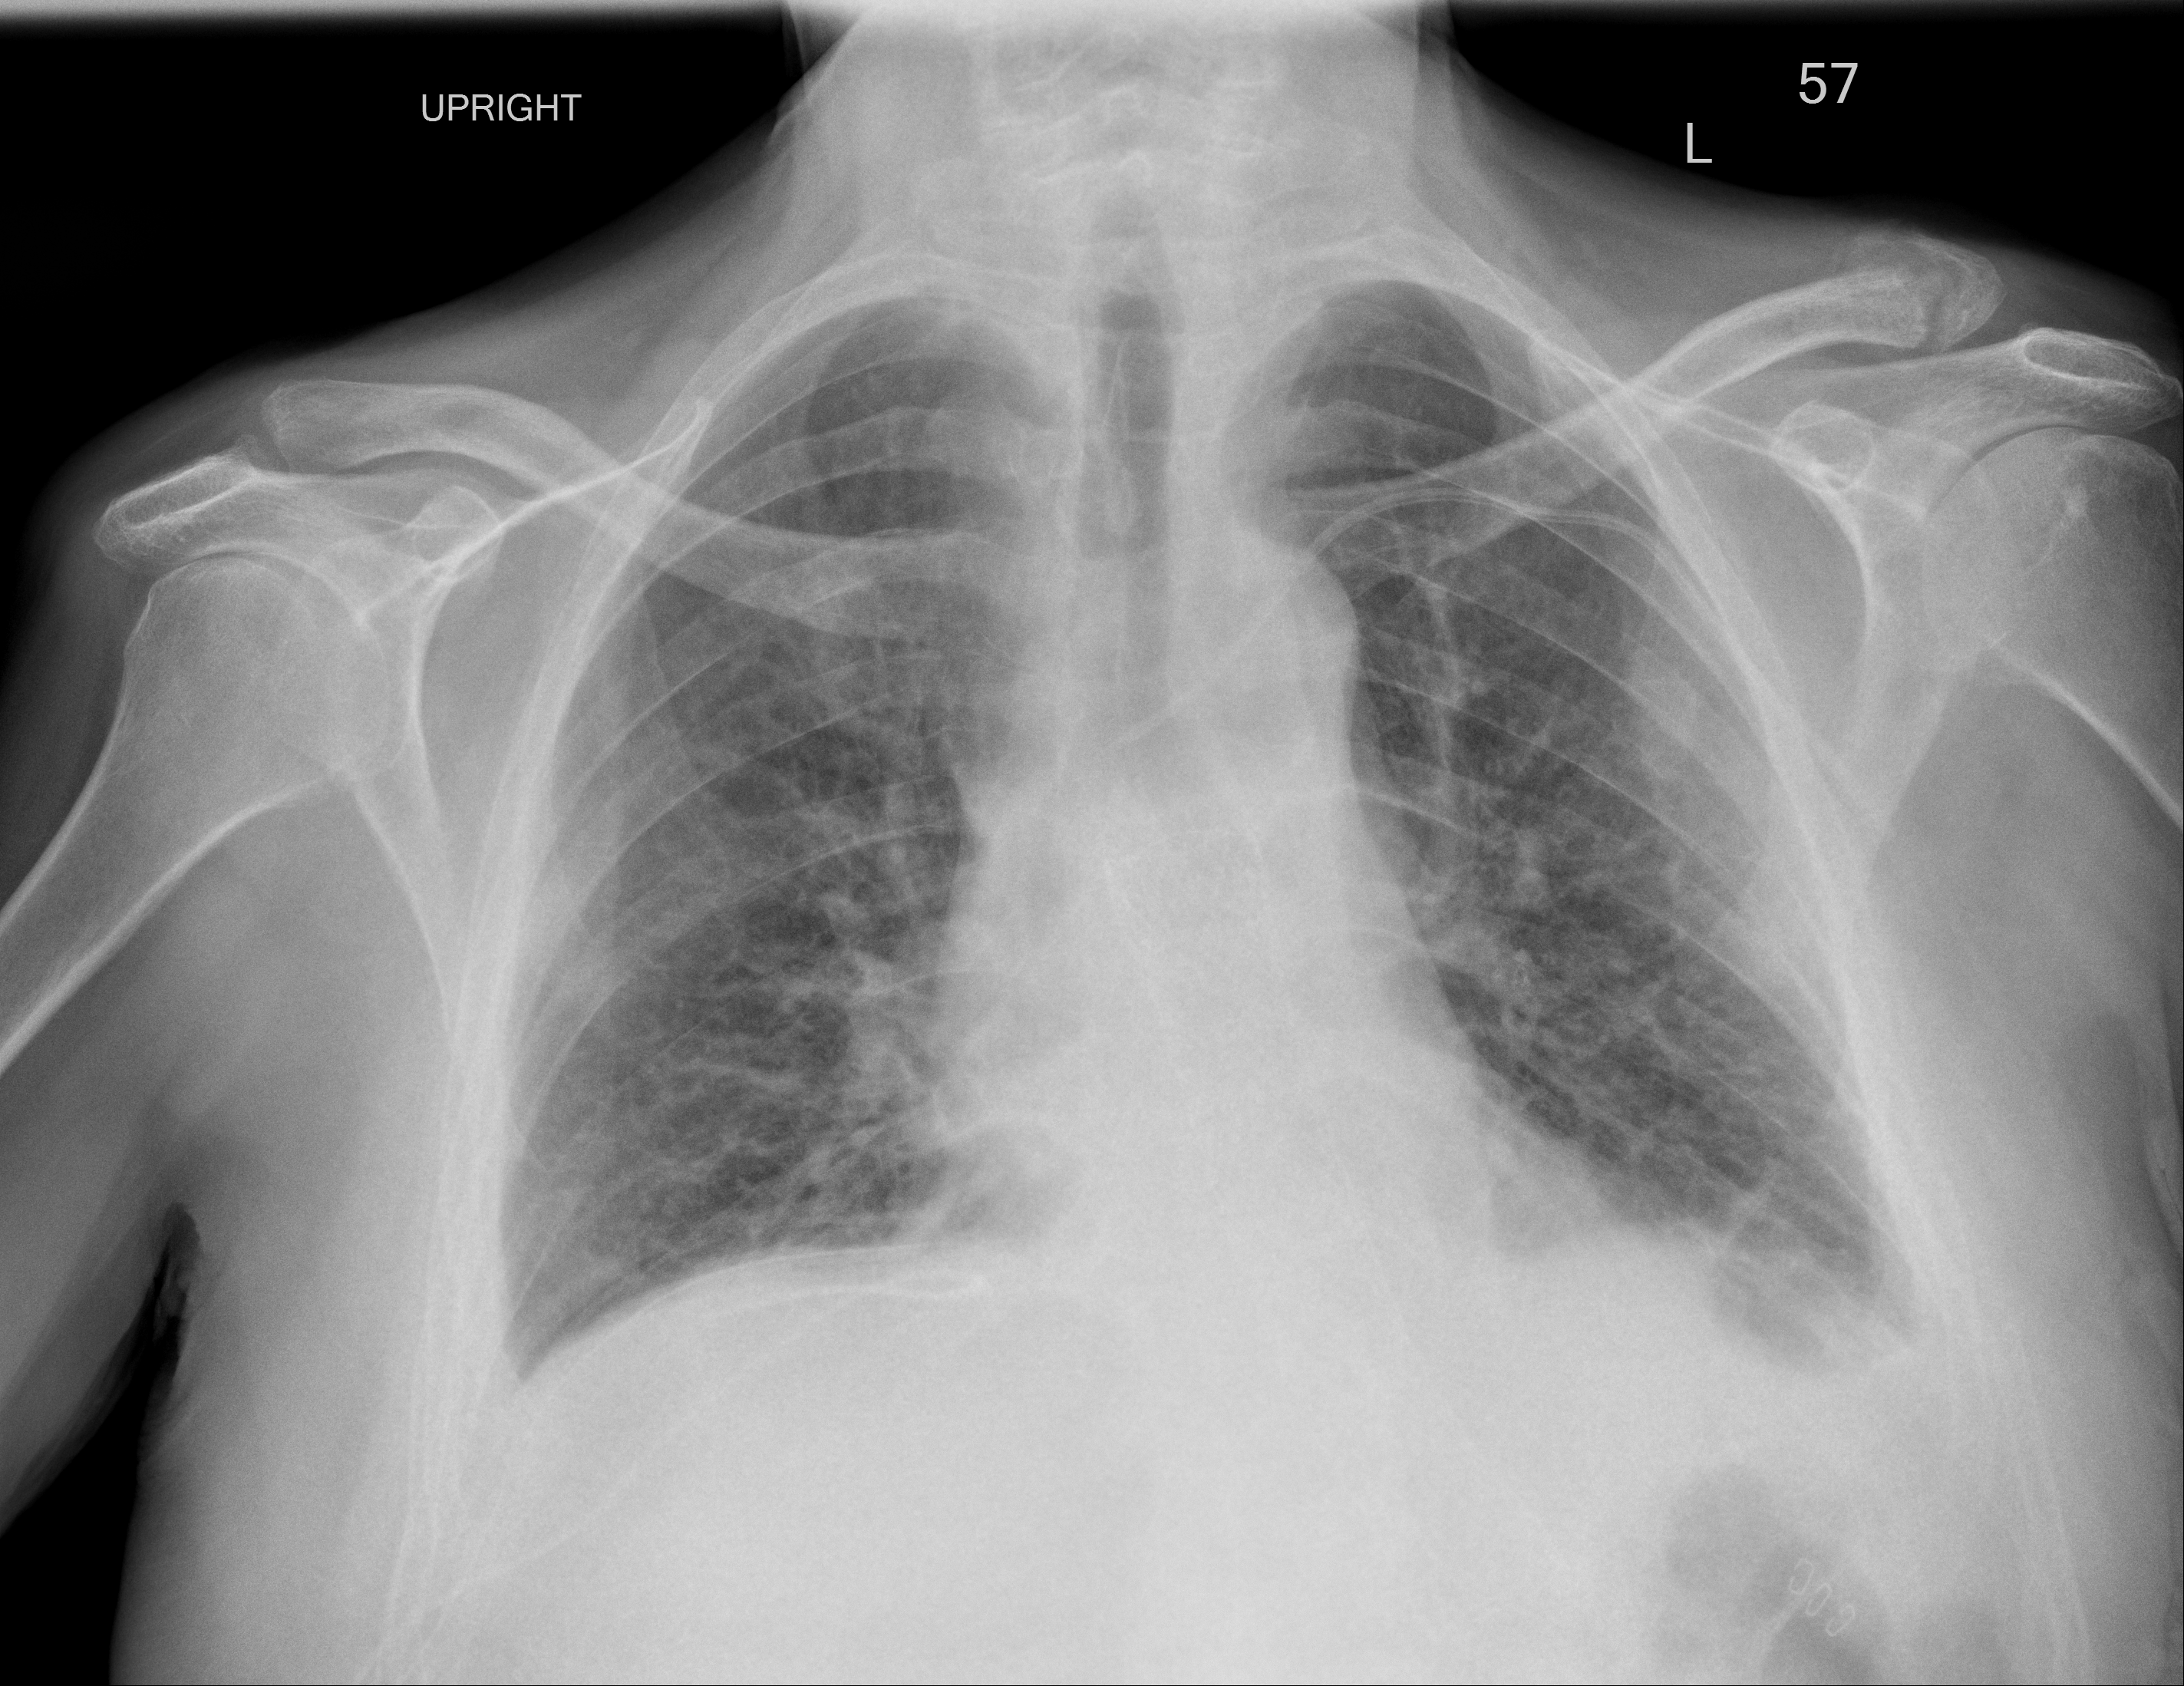
Chest X-ray (portable), AP projection. Male patient, age 64 years; COVID-19 (test-positive).
Radiologist's key findings for this exam: Small left pleural effusion. Mild bibasilar atelectatic changes, improving.